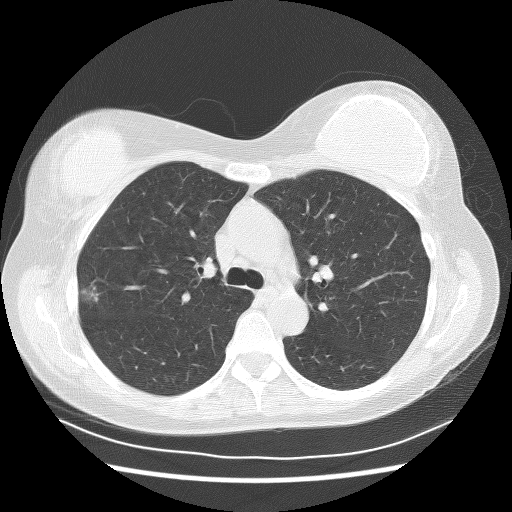
Chest CT (low-dose screening protocol), one axial image. Baseline annual screen. Lung window (W 1500 / L -600 HU). 2.5 mm slice thickness. 120 kVp. 512 × 512 image matrix. Female participant, aged 58 years at enrolment. Former smoker at enrolment.
Lesion marked by an expert reader, bounding box [x1, y1, x2, y2] px = [67, 272, 110, 312]. The screening reader recorded 2 non-calcified nodules or masses ≥4 mm on this exam (right upper lobe, right upper lobe); which of them this box marks is not recorded. Official screen result: positive, change unspecified: nodule(s) >= 4 mm or enlarging nodule(s), mass(es), or other non-specific abnormalities suspicious for lung cancer.